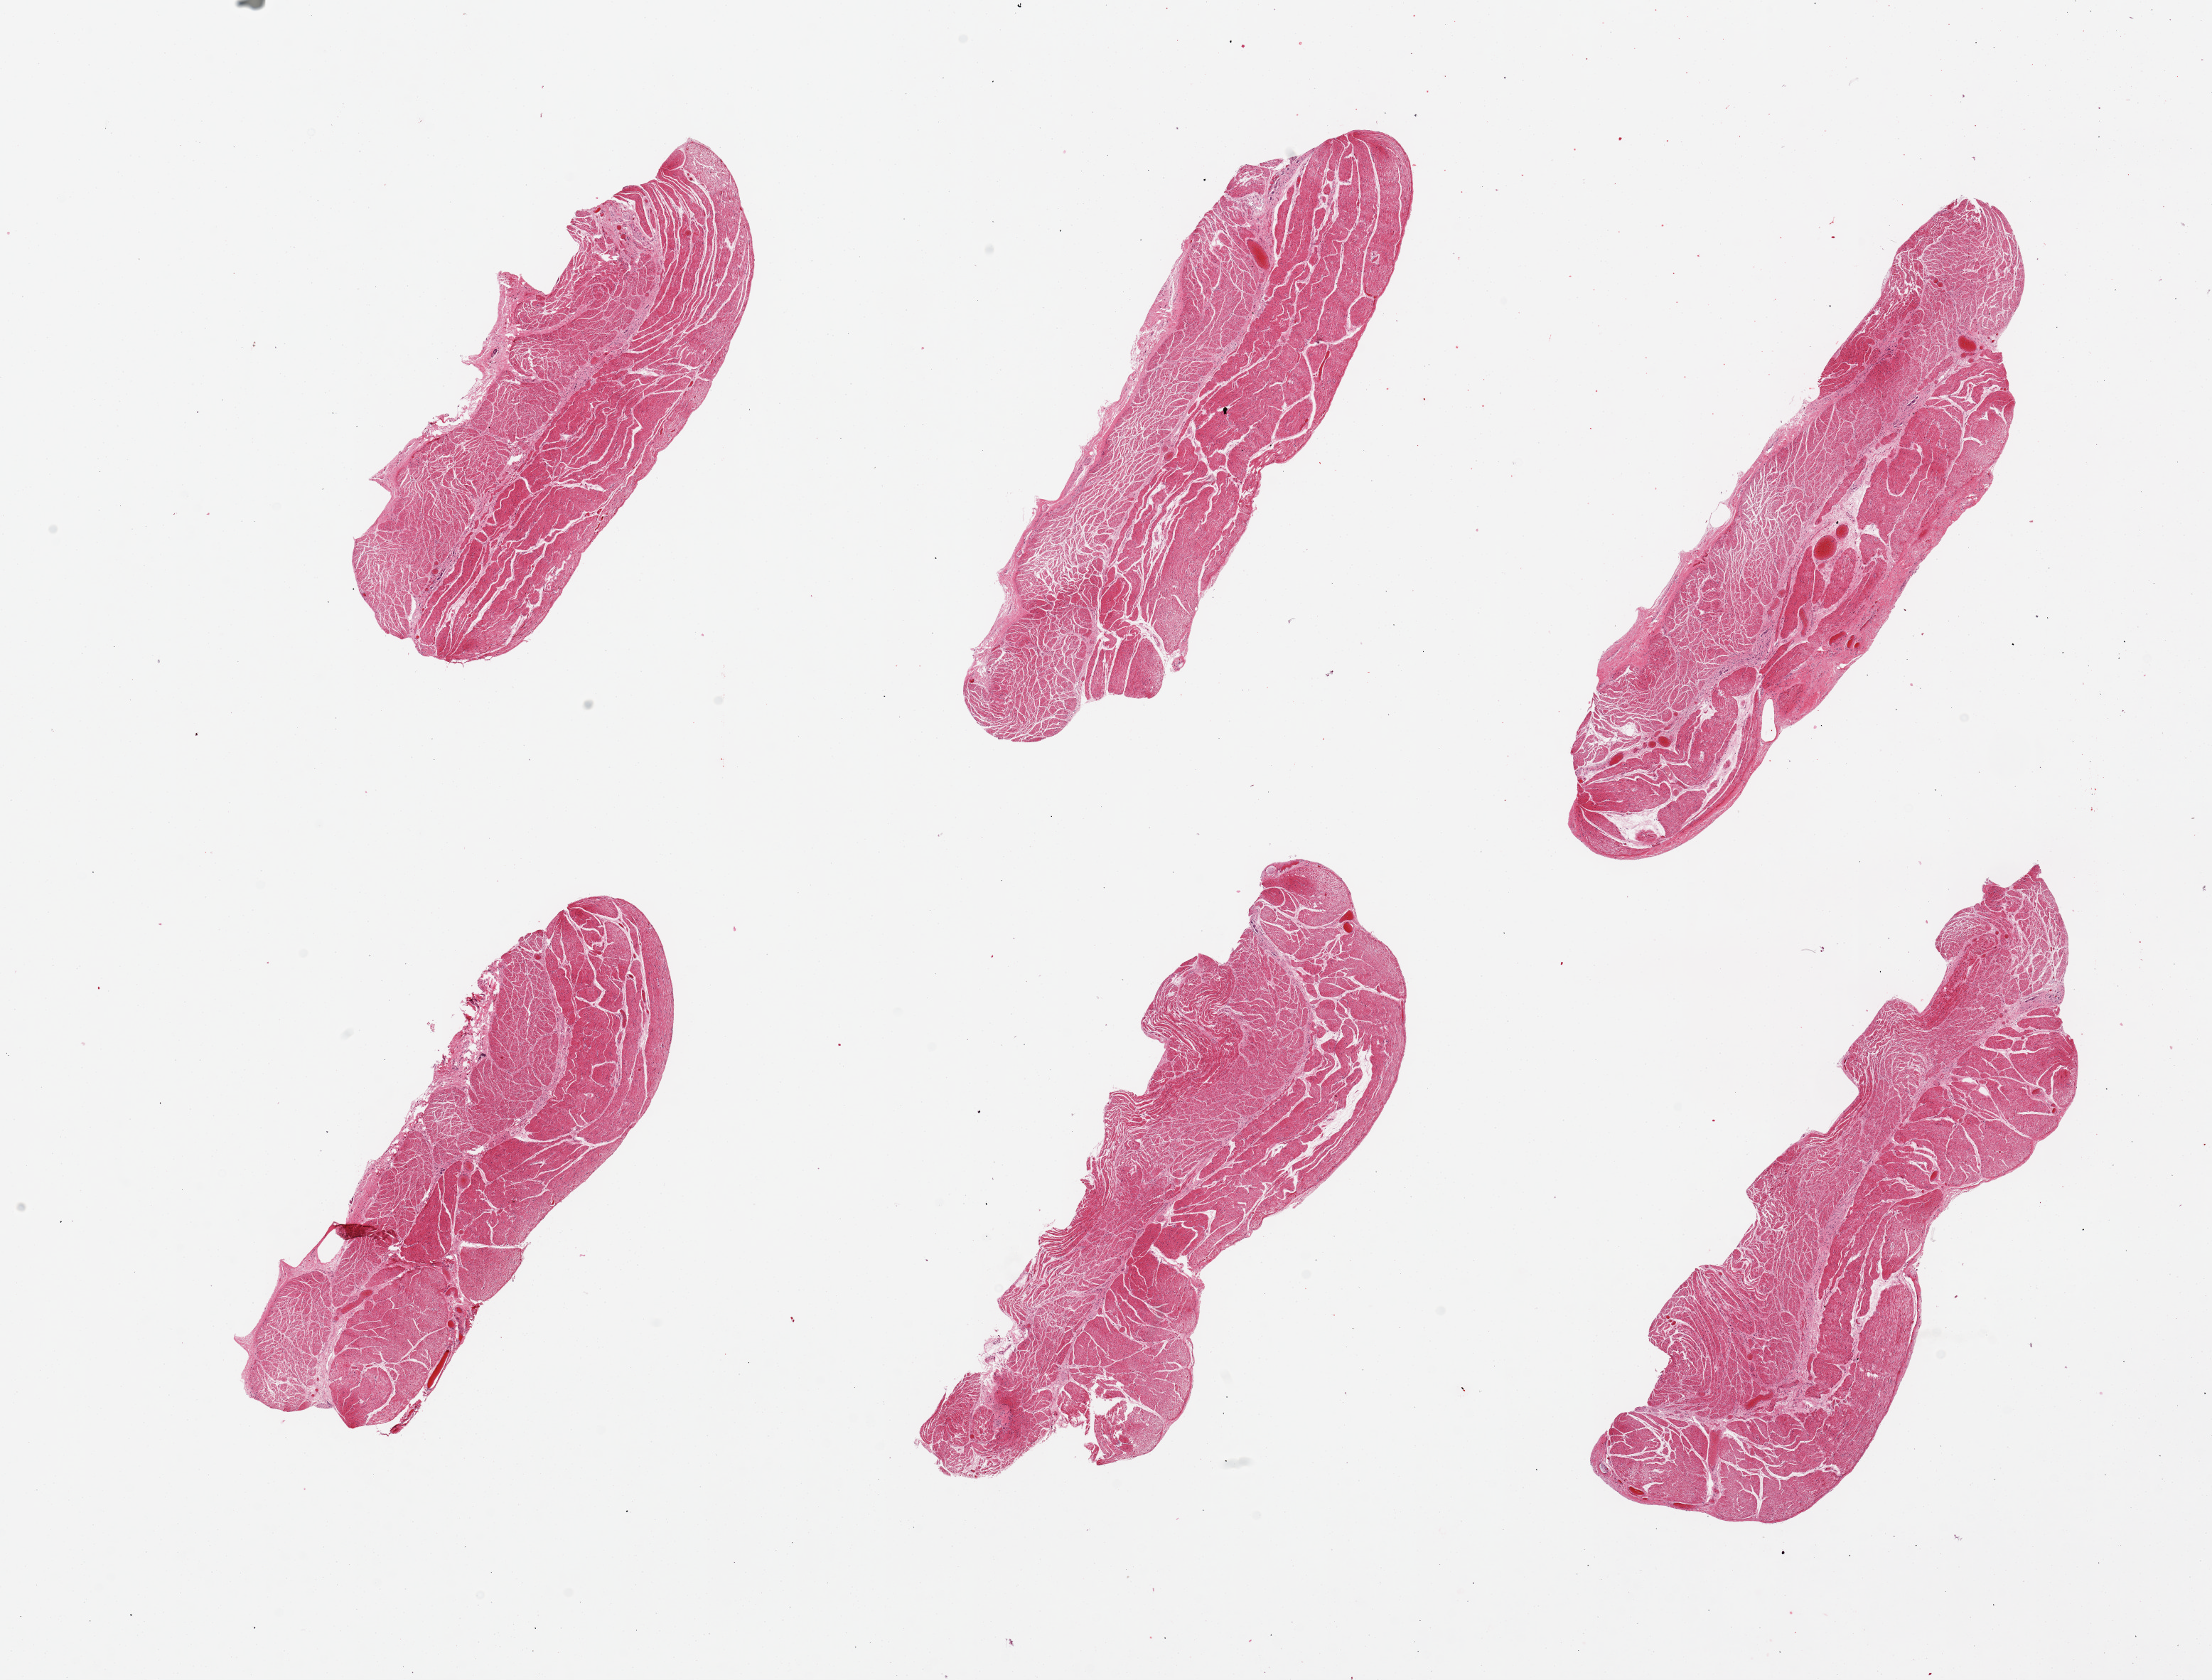
Digitized H&E-stained section — a low-resolution overview of the entire scanned area, about 24.6 x 18.7 mm (from a 20x scan), PAXgene-fixed paraffin-embedded (PFPE) section, sampled site (target tissue): esophageal muscle, tissue donor sample. Female donor.
Review note (as recorded): 6 pieces, all muscularis, good specimens.